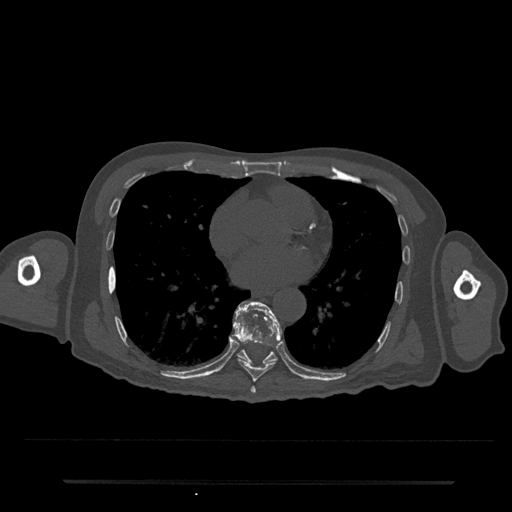
CT including the spine, one axial slice; slice 401 of 797 in the series (ordered by position); reconstruction kernel Br40s/3; 120 kVp; bone window (W 1800 / L 400 HU); 0.5 mm slice thickness; 512 × 512 image matrix, field of view 427 × 427 mm. Patient: male, 74 years. From the clinical record (not read from this slice): primary cancer: prostate.
Annotated regions visible in this slice (semi-automatic segmentation, software-assisted and operator-edited):
- T7 vertebra: bounding box (x1, y1, x2, y2) in pixels: (250, 386, 256, 394)
- T8 vertebra: (233, 301, 282, 382)
- T9 vertebra: (234, 303, 282, 364)